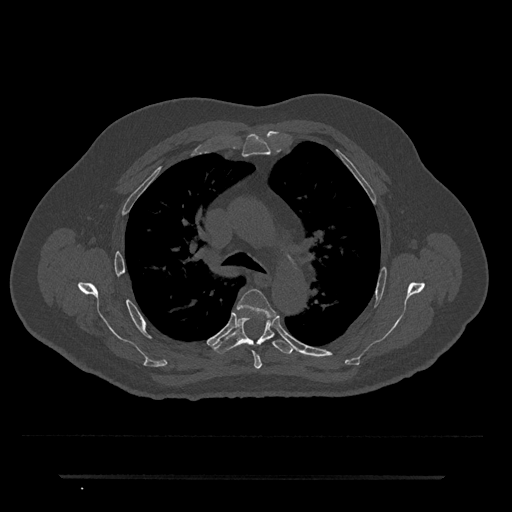
CT including the spine, one axial slice. Position 502 of 797 along the scan axis. Bone window (W 1800 / L 400 HU). 0.5 mm slice thickness. 512 × 512 image matrix, field of view 437 × 437 mm. Patient: male, 69 years. From the clinical record (not read from this slice): primary cancer: prostate.
Structures marked on this image (semi-automatically segmented with operator editing):
- T4 vertebra: bounding box [x1, y1, x2, y2] px = [237, 289, 277, 369]
- T5 vertebra: [212, 317, 295, 354]